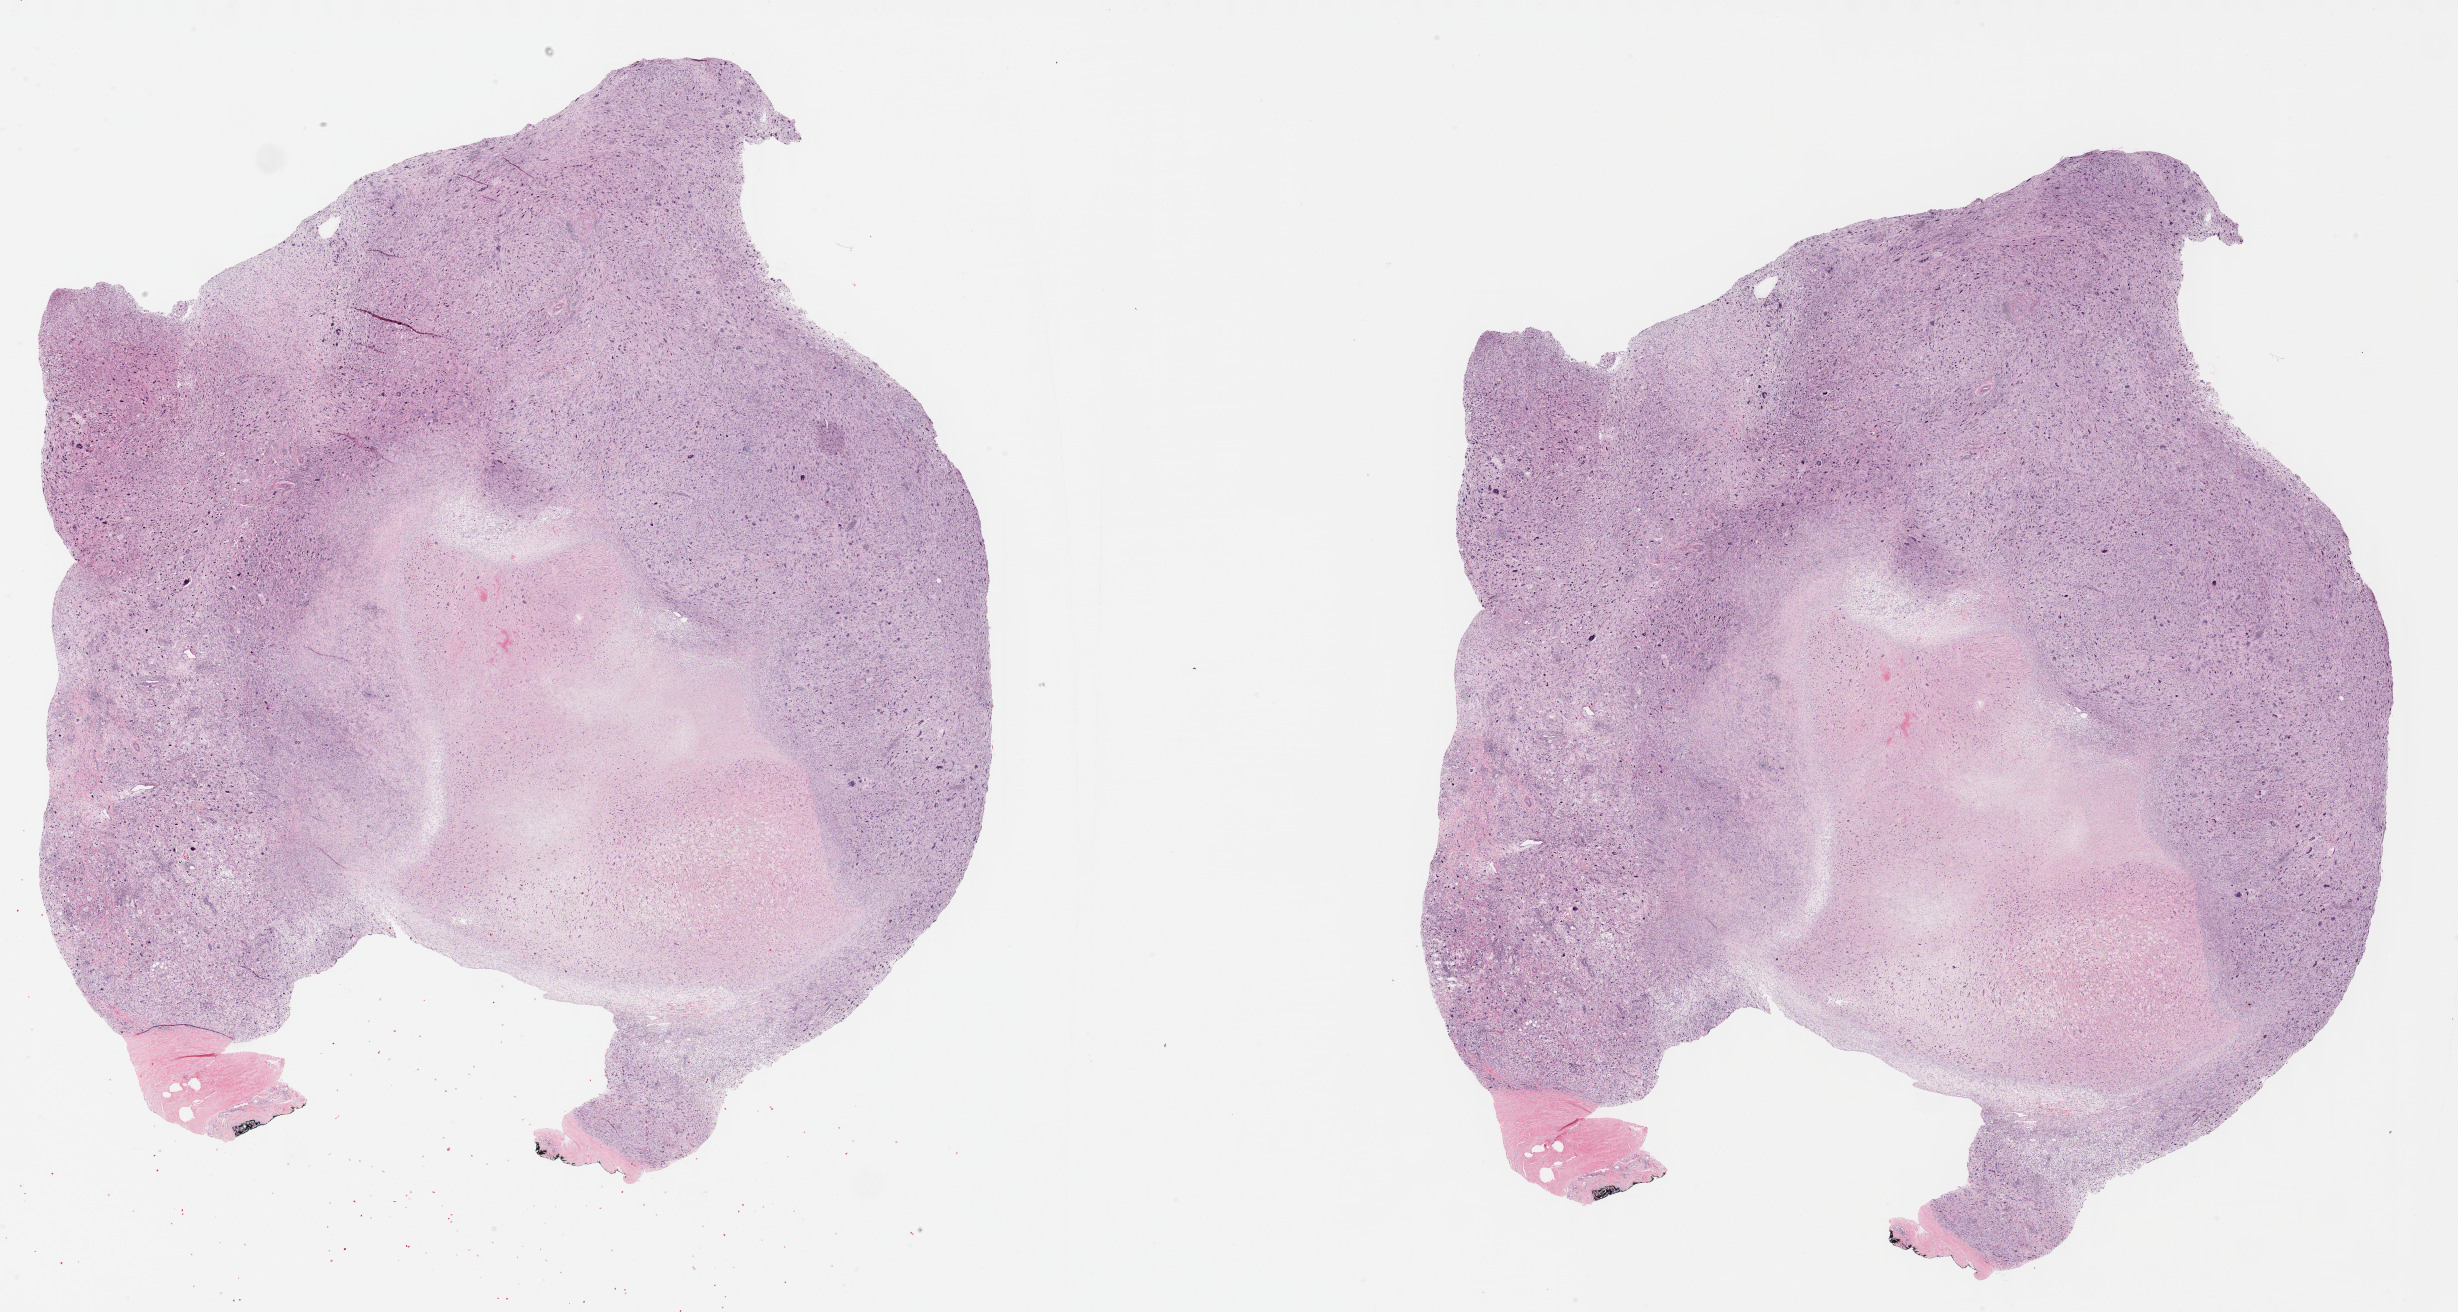
H&E whole-slide image — shown as a low-resolution overview of the whole scanned area (about 39.7 x 21.2 mm, from a 40x scan); formalin-fixed paraffin-embedded (FFPE) diagnostic section; sample: primary tumour, connective, subcutaneous and other soft tissues. Female patient; age at initial diagnosis 67 years.
Pathologic diagnosis: Undifferentiated sarcoma.